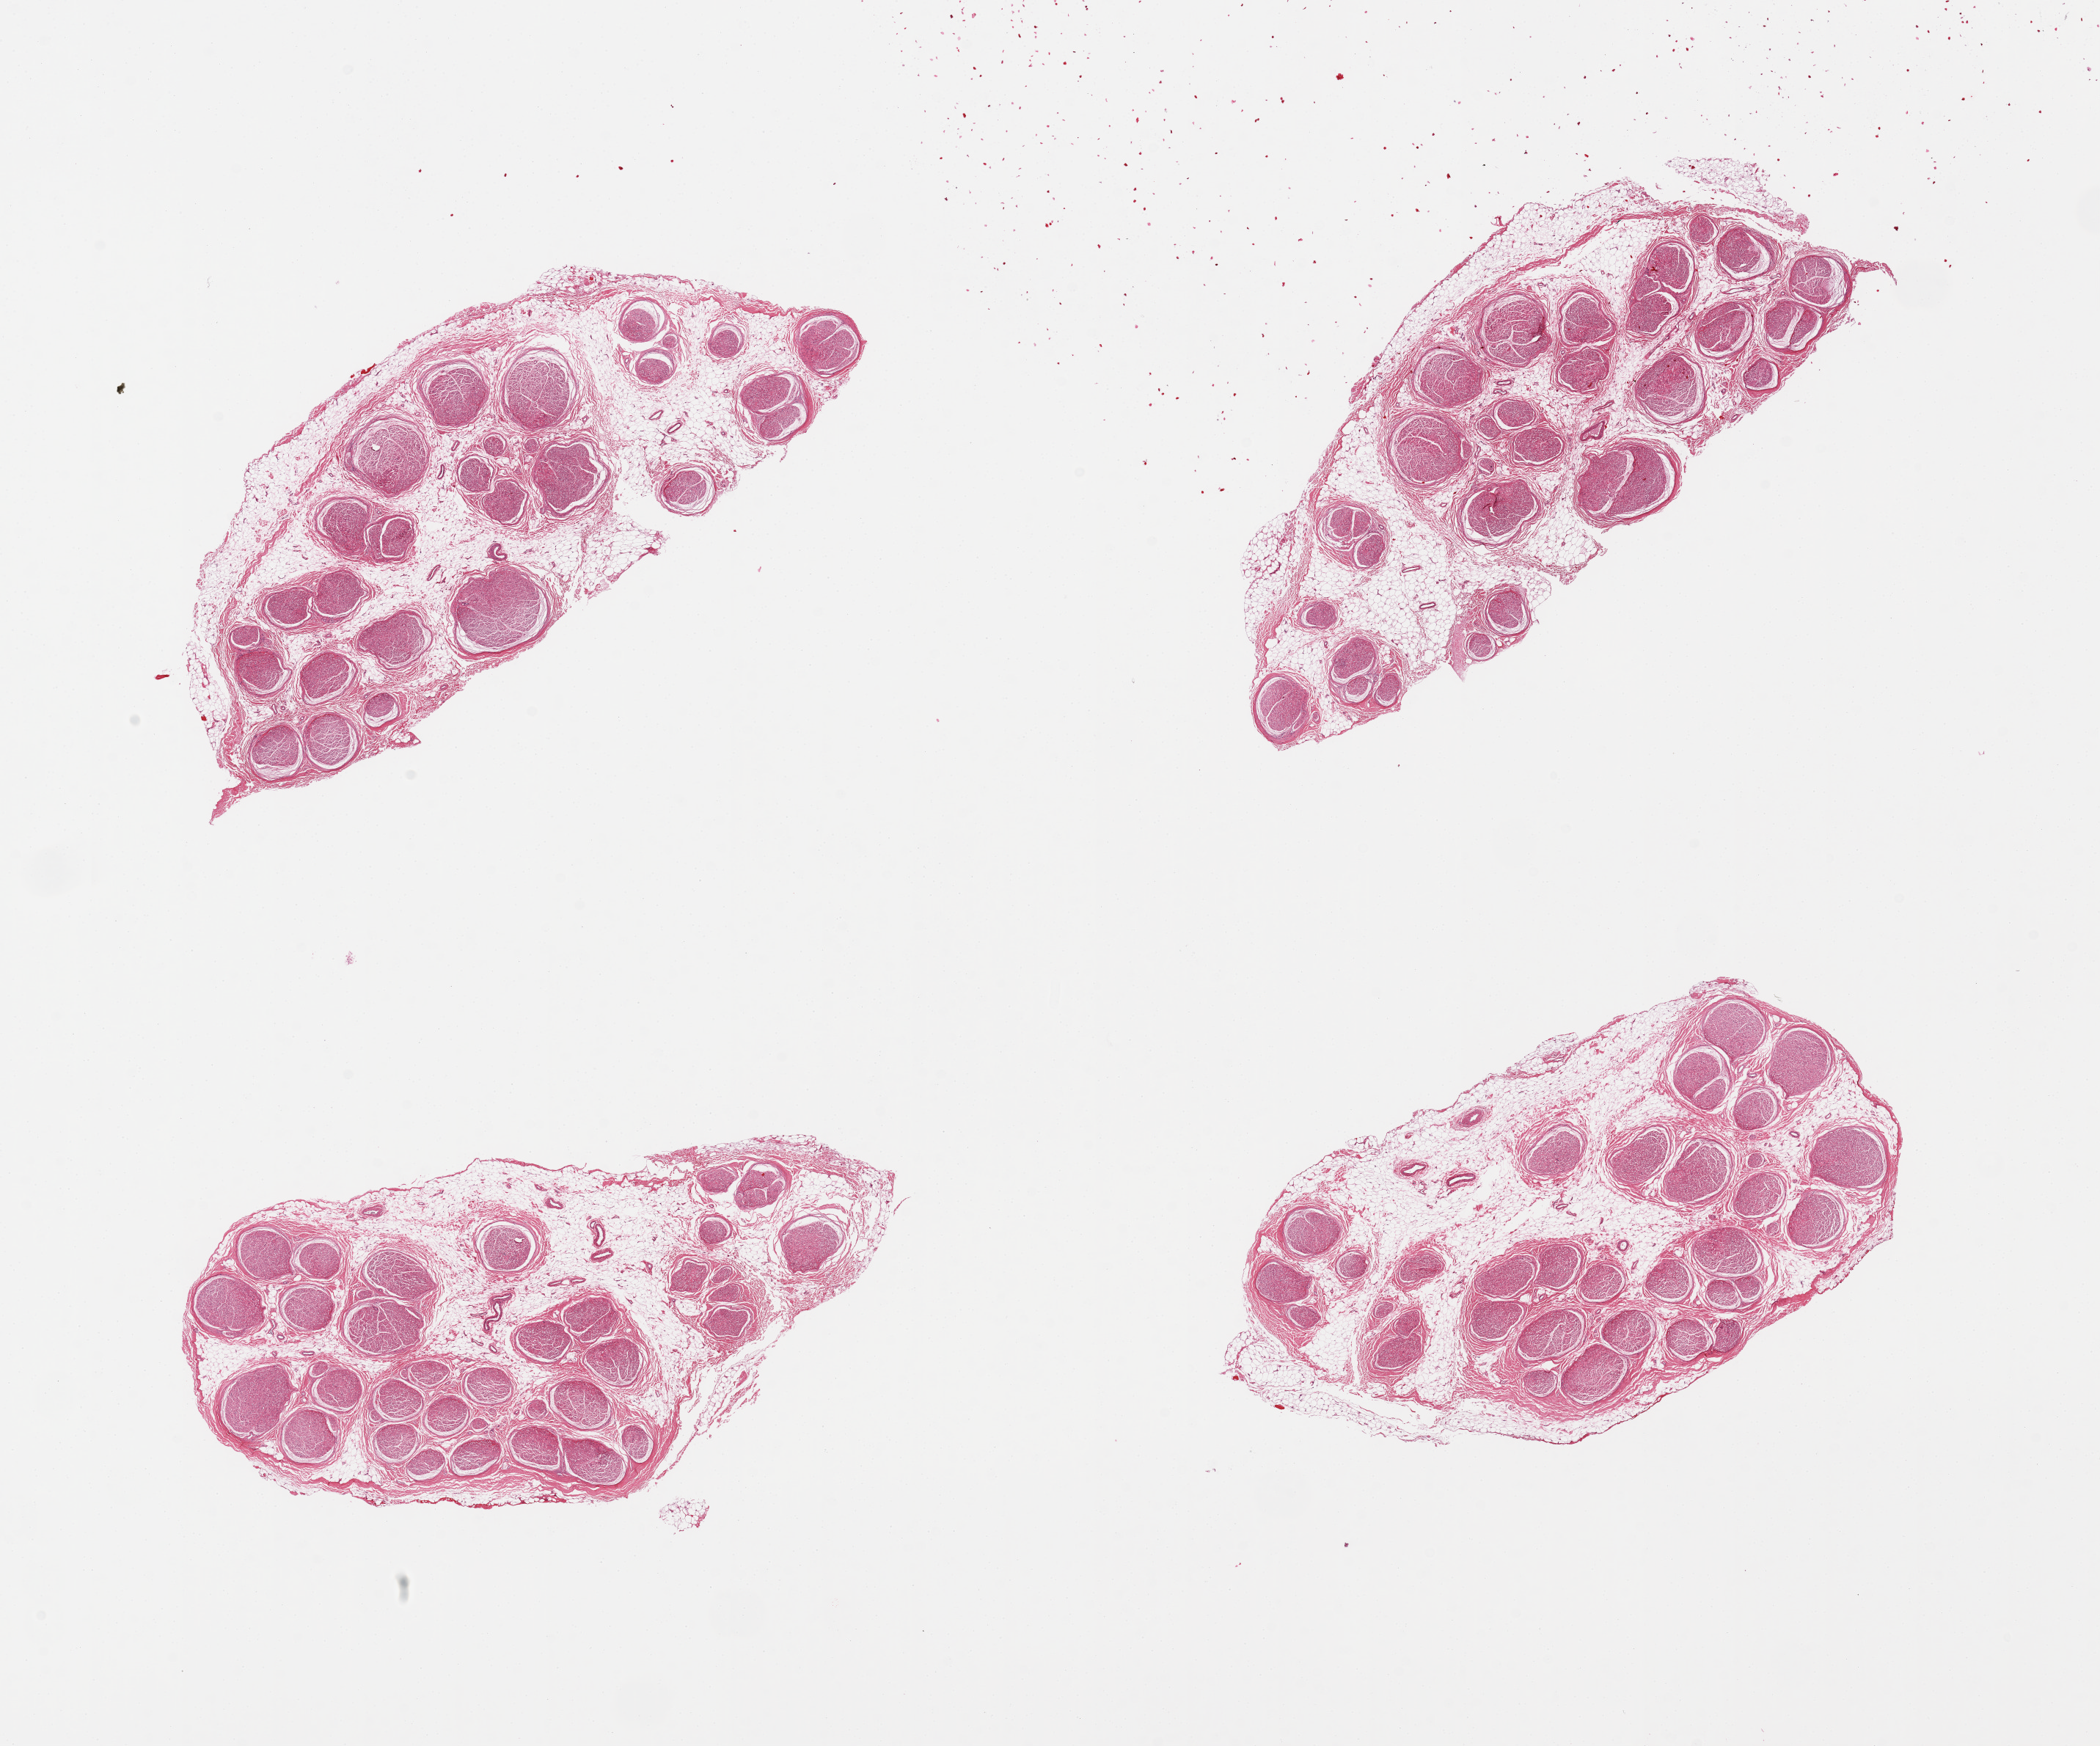
Whole-slide image, H&E stain, brightfield, a low-resolution overview of the entire scanned area, about 22.6 x 18.8 mm (slide scanned at 20x), PAXgene-fixed, paraffin-embedded tissue, target tissue: tibial nerve, tissue donor sample. Donor sex: male.
* review note (as recorded): 4 pieces, up to ~40-50% fat (attached and internal)